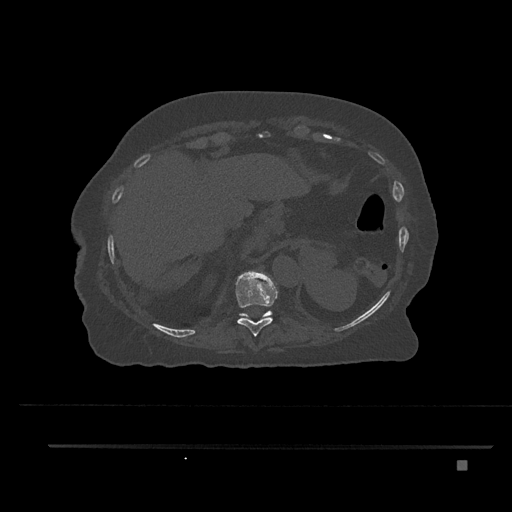
CT including the spine, one axial slice; slice 346 of 797 in the series (ordered by position); reconstruction kernel Br40s/3; 120 kVp; bone window (W 1800 / L 400 HU); 0.5 mm slice thickness; 512 × 512 image matrix, field of view 437 × 437 mm. Patient: female, 76 years. Case-level facts recorded for this patient, not image findings: primary cancer: lung; vertebrae with lytic lesions (as recorded): T11, L3.
Annotated regions visible in this slice (semi-automatic segmentation, software-assisted and operator-edited):
- T10 vertebra: box from (x=235, y=270) to (x=278, y=336) px
- T11 vertebra: (x=239, y=311)–(x=272, y=319)